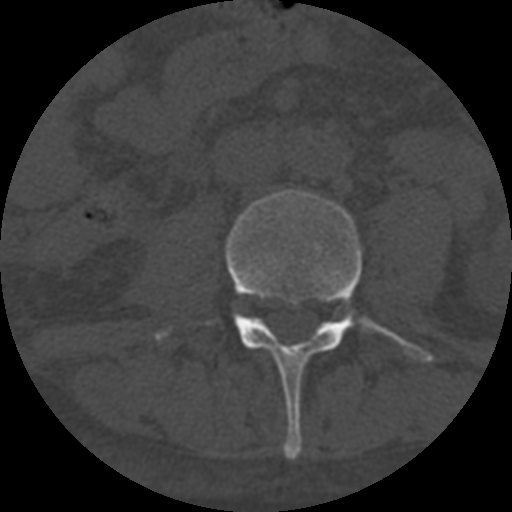
CT including the spine, one axial slice; position 231 of 708 along the scan axis; reconstruction kernel STANDARD; 120 kVp; one of 3 acquisitions stored at this slice position; bone window (W 1800 / L 400 HU); 1.25 mm slice thickness; 512 × 512 image matrix. Patient age 55 years. From the clinical record (not read from this slice): primary cancer: colon.
Outlined on this slice (semi-automatically segmented with operator editing):
- L3 vertebra: bounding box (x1, y1, x2, y2) in pixels: (154, 190, 433, 460)